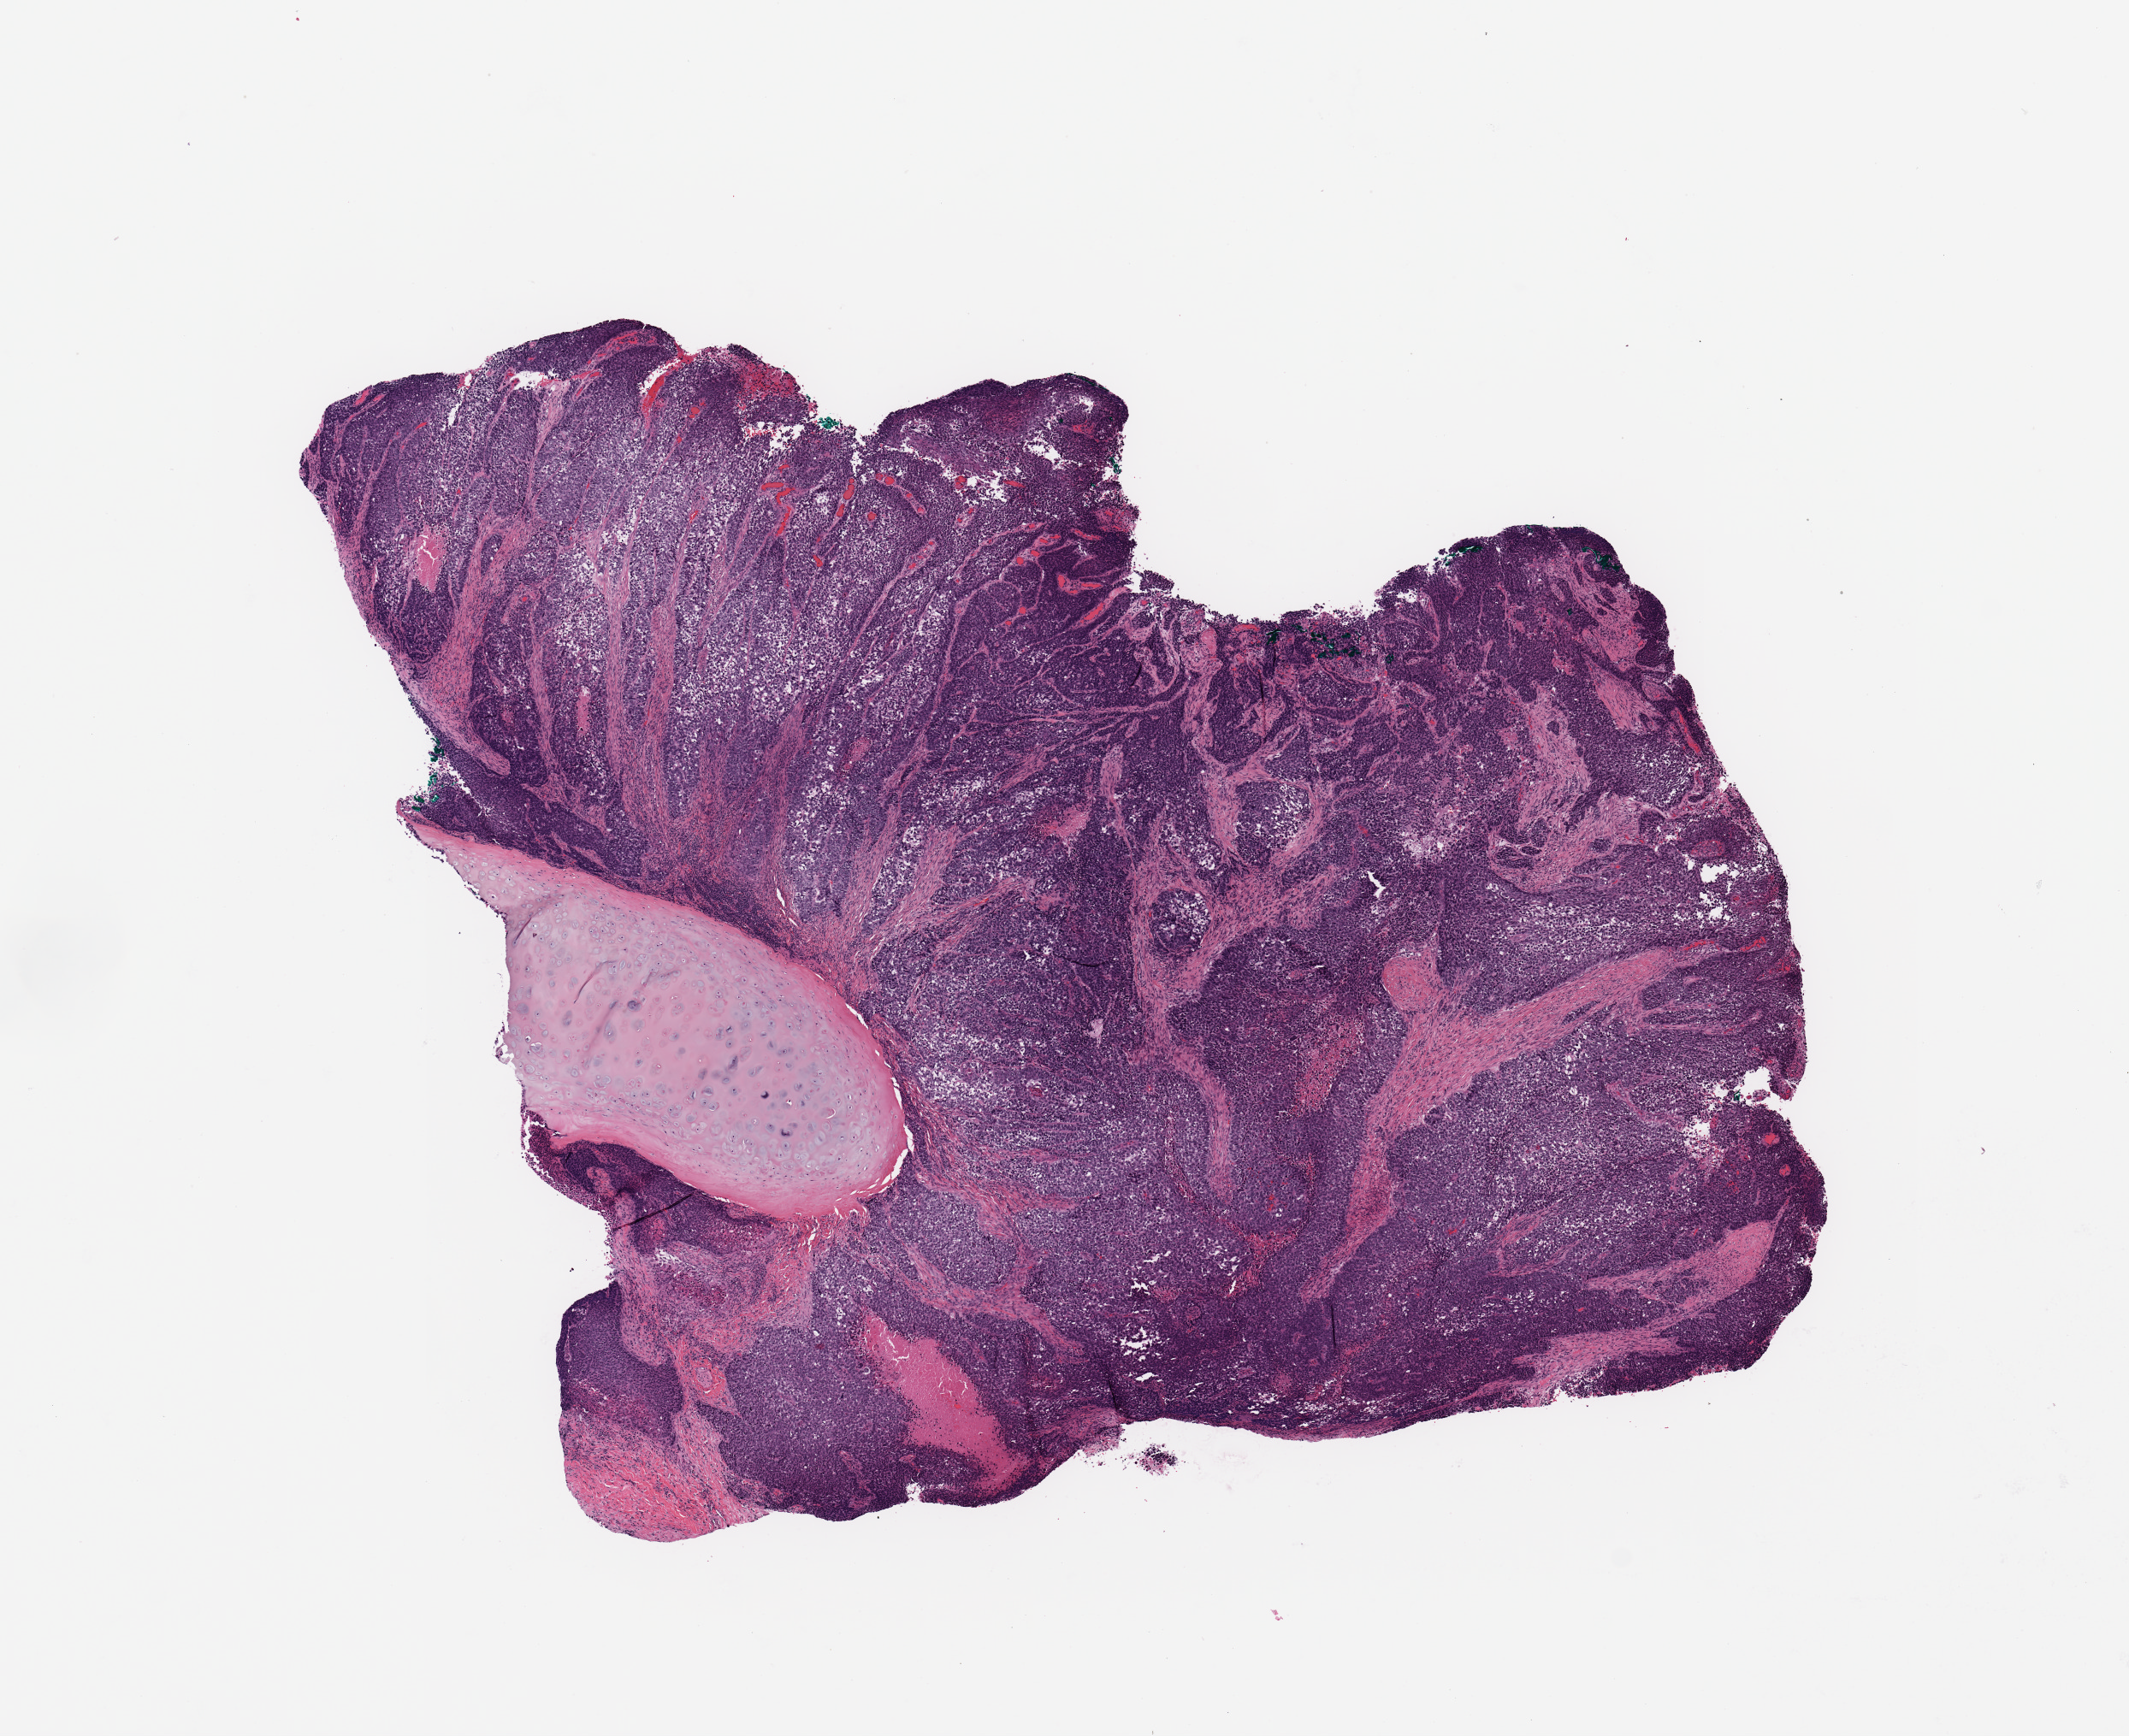
Whole-slide histology image, H&E-stained, shown as a low-resolution overview of the whole scanned area (about 9.8 x 8.0 mm, from a 20x scan). Tumour tissue sample, lung. 63-year-old male patient. Histologic grade: G2 (moderately differentiated).
Primary tumour site (as recorded): right upper lobe. Histologic diagnosis: Squamous cell carcinoma, NOS. AJCC pathologic stage: IIA.